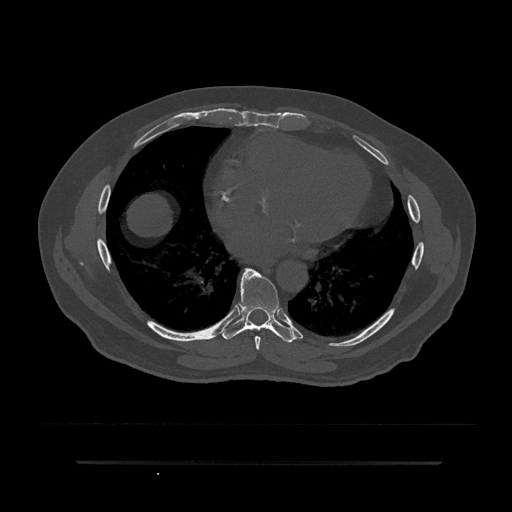
CT including the spine, one axial slice. Slice 443 of 797 in the series (ordered by position). Reconstruction kernel Br40s/3. 120 kVp. Bone window (W 1800 / L 400 HU). 0.5 mm slice thickness. 512 × 512 image matrix, field of view 464 × 464 mm. Male patient, age 59 years. Case-level facts recorded for this patient, not image findings: primary cancer: bile ducts; vertebrae with lytic lesions (as recorded): T10.
Outlined on this slice (semi-automatically segmented with operator editing):
- T7 vertebra: box from (x=242, y=268) to (x=261, y=350) px
- T8 vertebra: (x=222, y=269)–(x=295, y=343)